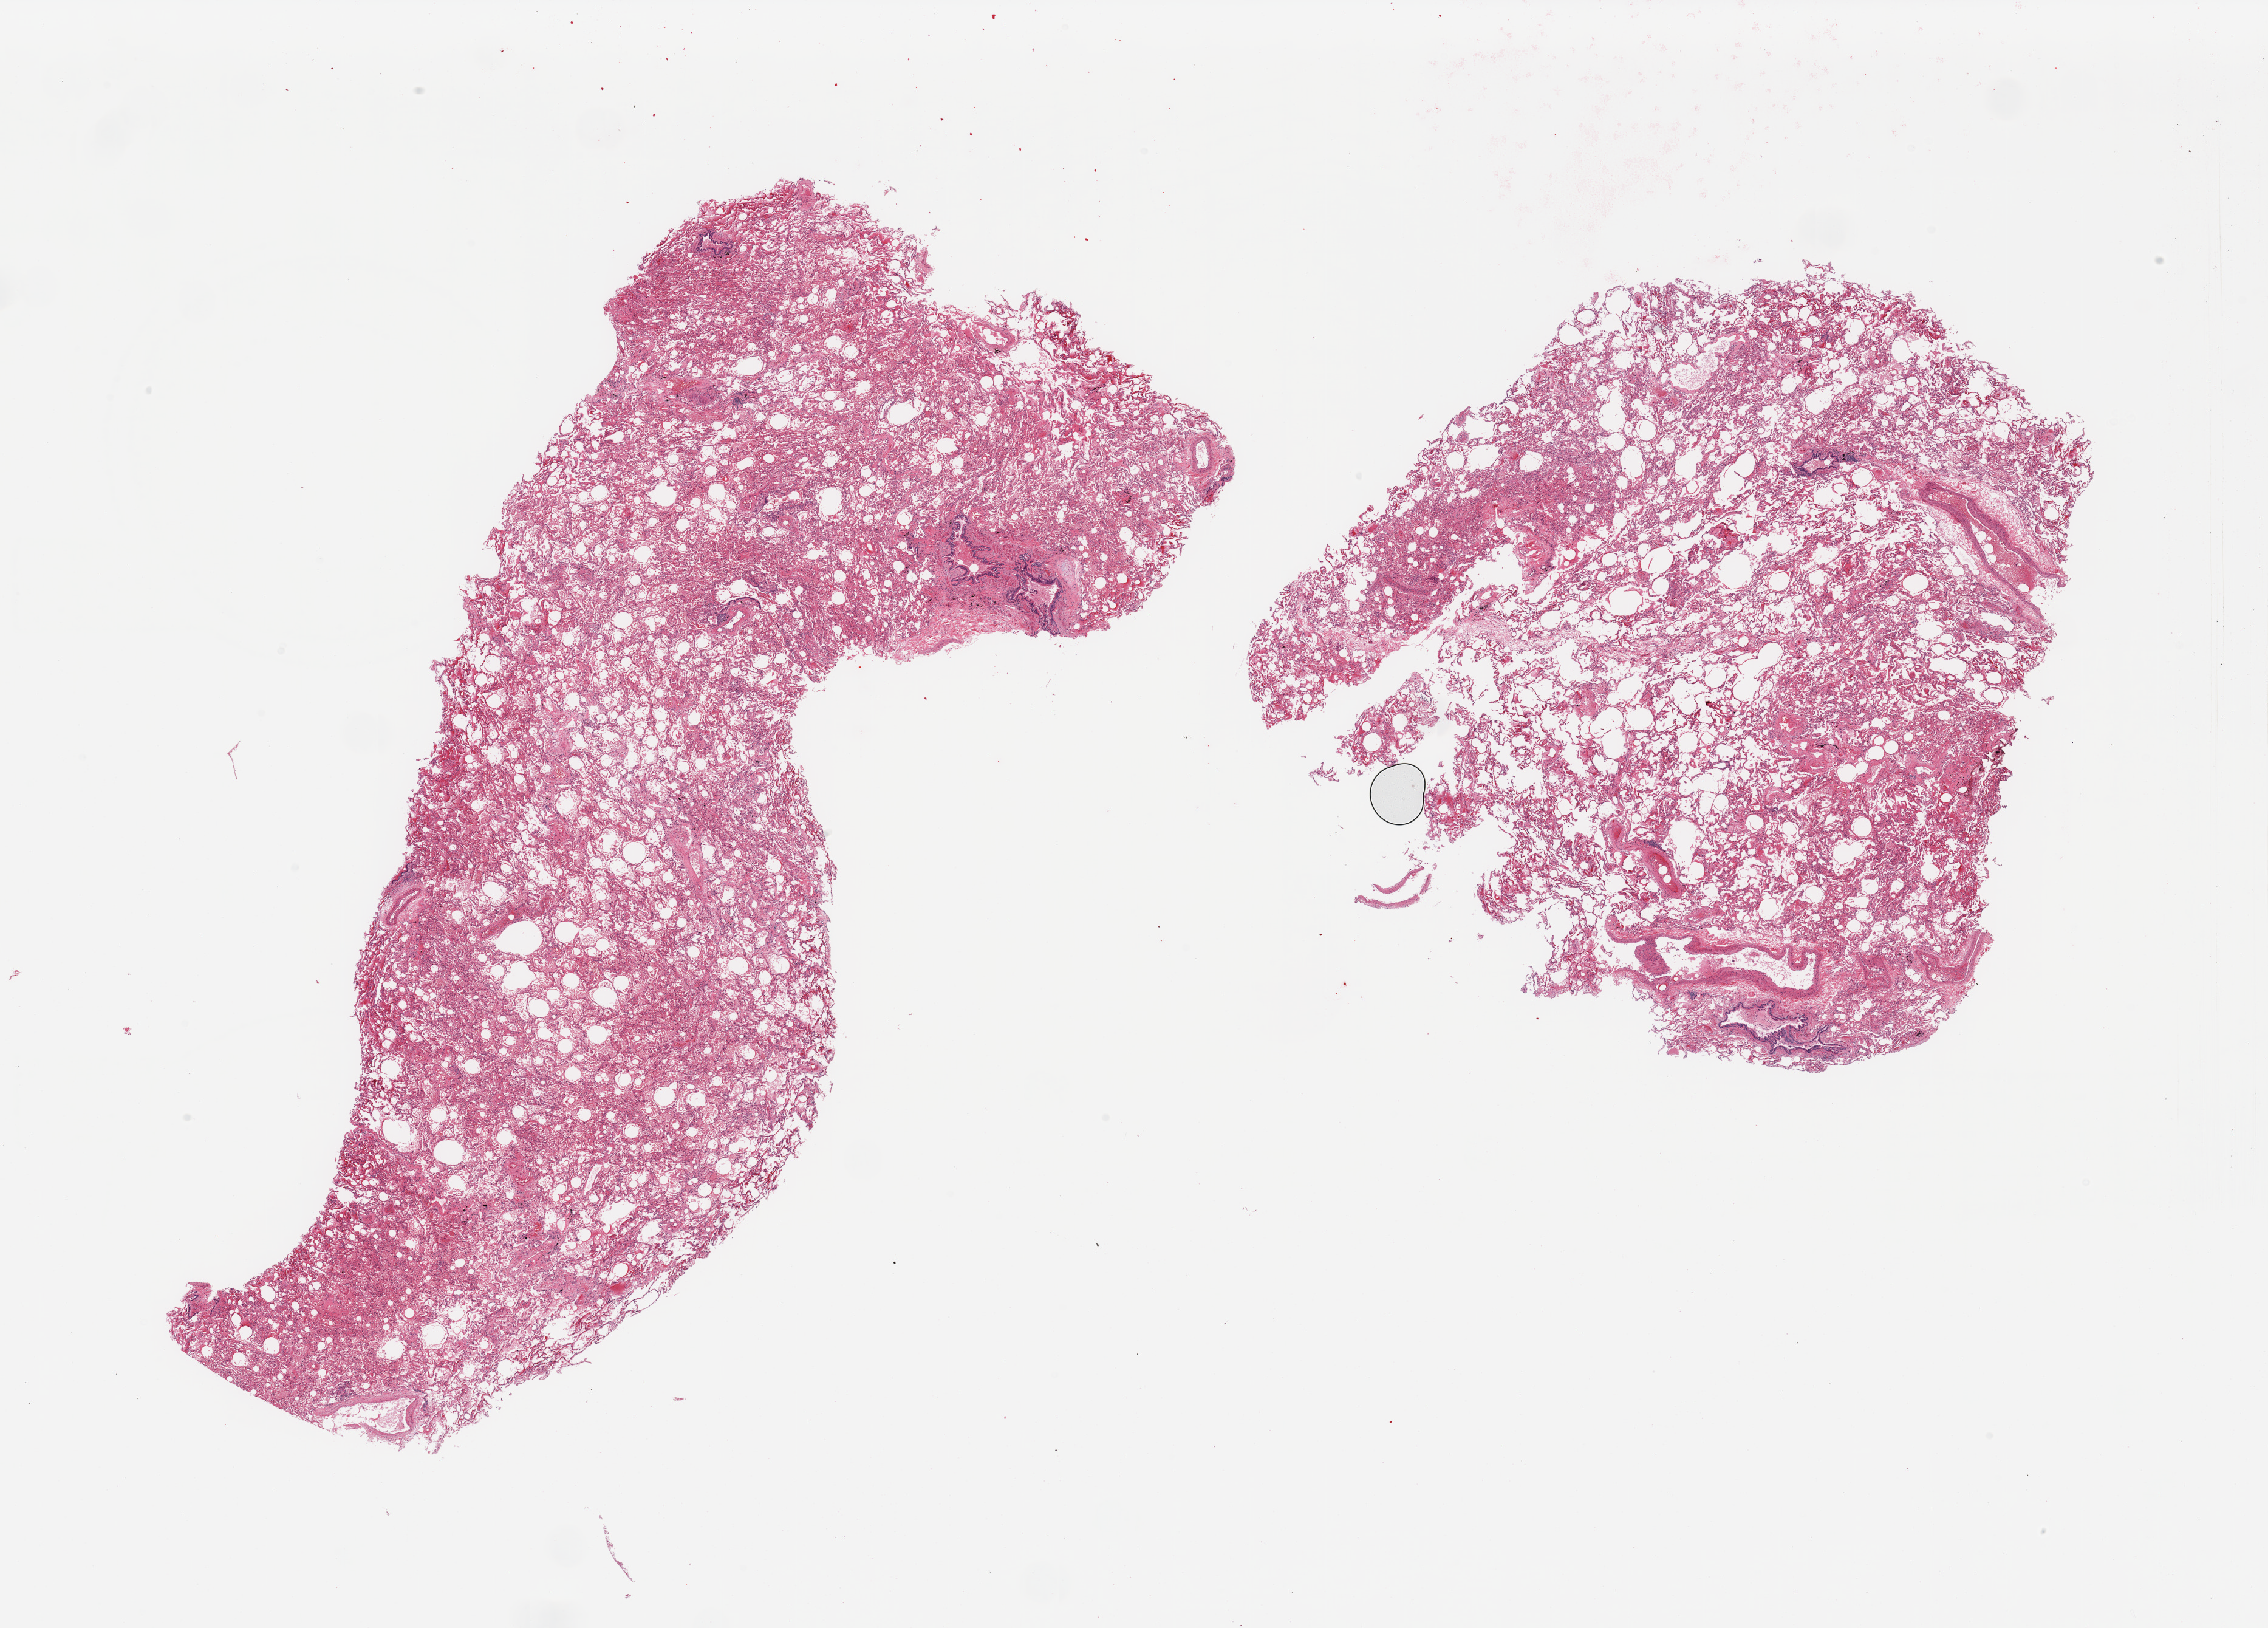
Digitized H&E-stained section — whole scanned area (about 29.5 x 21.2 mm) shown as a low-resolution overview; PAXgene-fixed paraffin-embedded (PFPE) section; target tissue: lung; donor tissue sample. Donor: male.
Review note (as recorded): 2 pieces, minimal congestion.